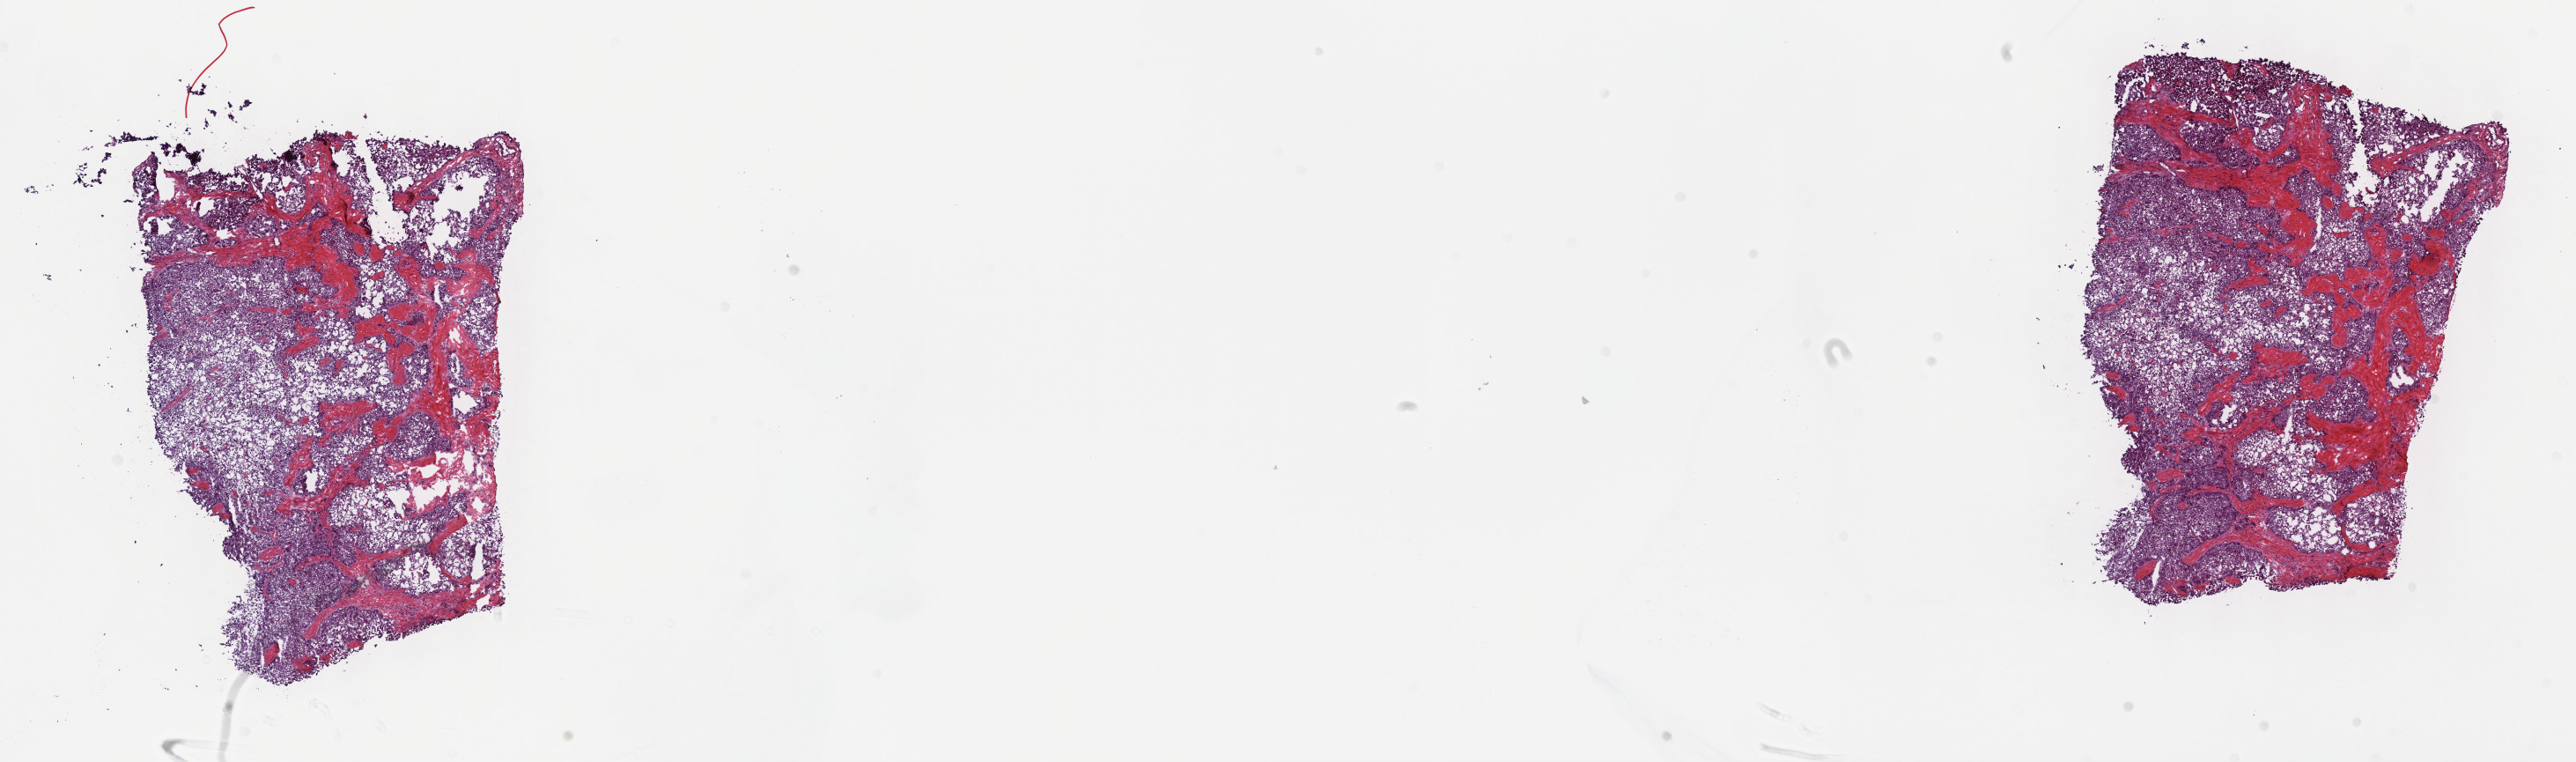
Hematoxylin and eosin (H&E) stained whole-slide image, a low-resolution overview of the entire scanned area, about 23.7 x 7.0 mm; frozen section from the top of the tissue portion; sample: primary tumour, liver. Male, age 73 years at initial diagnosis. Histologic grade: G2 (moderately differentiated). Composition of this section per pathologist review: tumour cells 80%, tumour nuclei 80%, normal cells 0%, stromal cells 20%, necrosis 0%. Inflammatory infiltration, as recorded: lymphocyte infiltration 2%, monocyte infiltration 1%, neutrophil infiltration 3%.
- diagnosis: Hepatocellular carcinoma, NOS
- AJCC pathologic stage: II (7th edition)